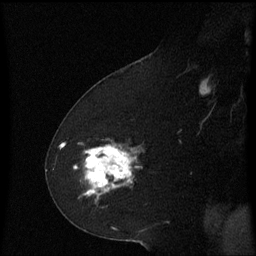
Breast MRI (dynamic contrast-enhanced), one sagittal slice. Slice 34 of 60 in the series (ordered by position). Dynamic contrast-enhanced series, image 2 of 3 at this slice position (ordered by acquisition). 1.5 T. TE 4.2 ms, TR 8.4 ms. 256 × 256 image matrix, field of view 200 × 200 mm. Patient: female, 60 years. From the clinical record (not read from this slice): setting: breast cancer imaged before/during neoadjuvant chemotherapy; receptor status: triple-negative.
Structures marked on this image (semi-automatic segmentation, software-assisted and operator-edited):
- analysis volume of interest (the breast-tissue region the enhancement analysis was run in; not a lesion): bounding box <74,142,143,209> (left, top, right, bottom; pixels)
- tumour enhancement mask (voxels above the 70 % enhancement threshold inside the analysis volume of interest): <86,146,137,195>